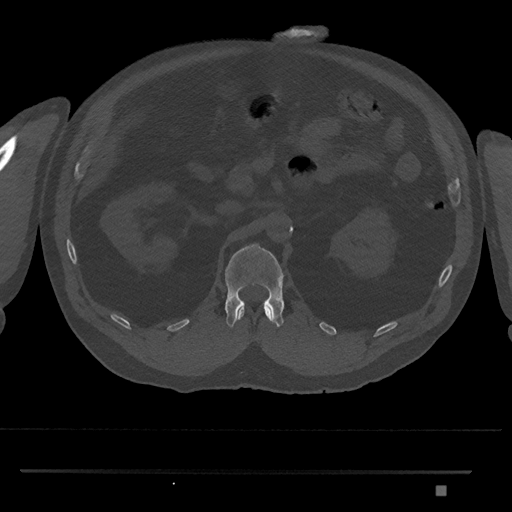
CT including the spine, one axial slice; slice 840 of 1134 in the series (ordered by position); 120 kVp; bone window (W 1800 / L 400 HU); 512 × 512 image matrix, field of view 429 × 429 mm. Male patient, age 65 years. Case-level facts recorded for this patient, not image findings: primary cancer: prostate.
Structures marked on this image (semi-automatically segmented with operator editing):
- L1 vertebra: bounding box <225,244,285,328> (left, top, right, bottom; pixels)
- T12 vertebra: <236,307,271,321>